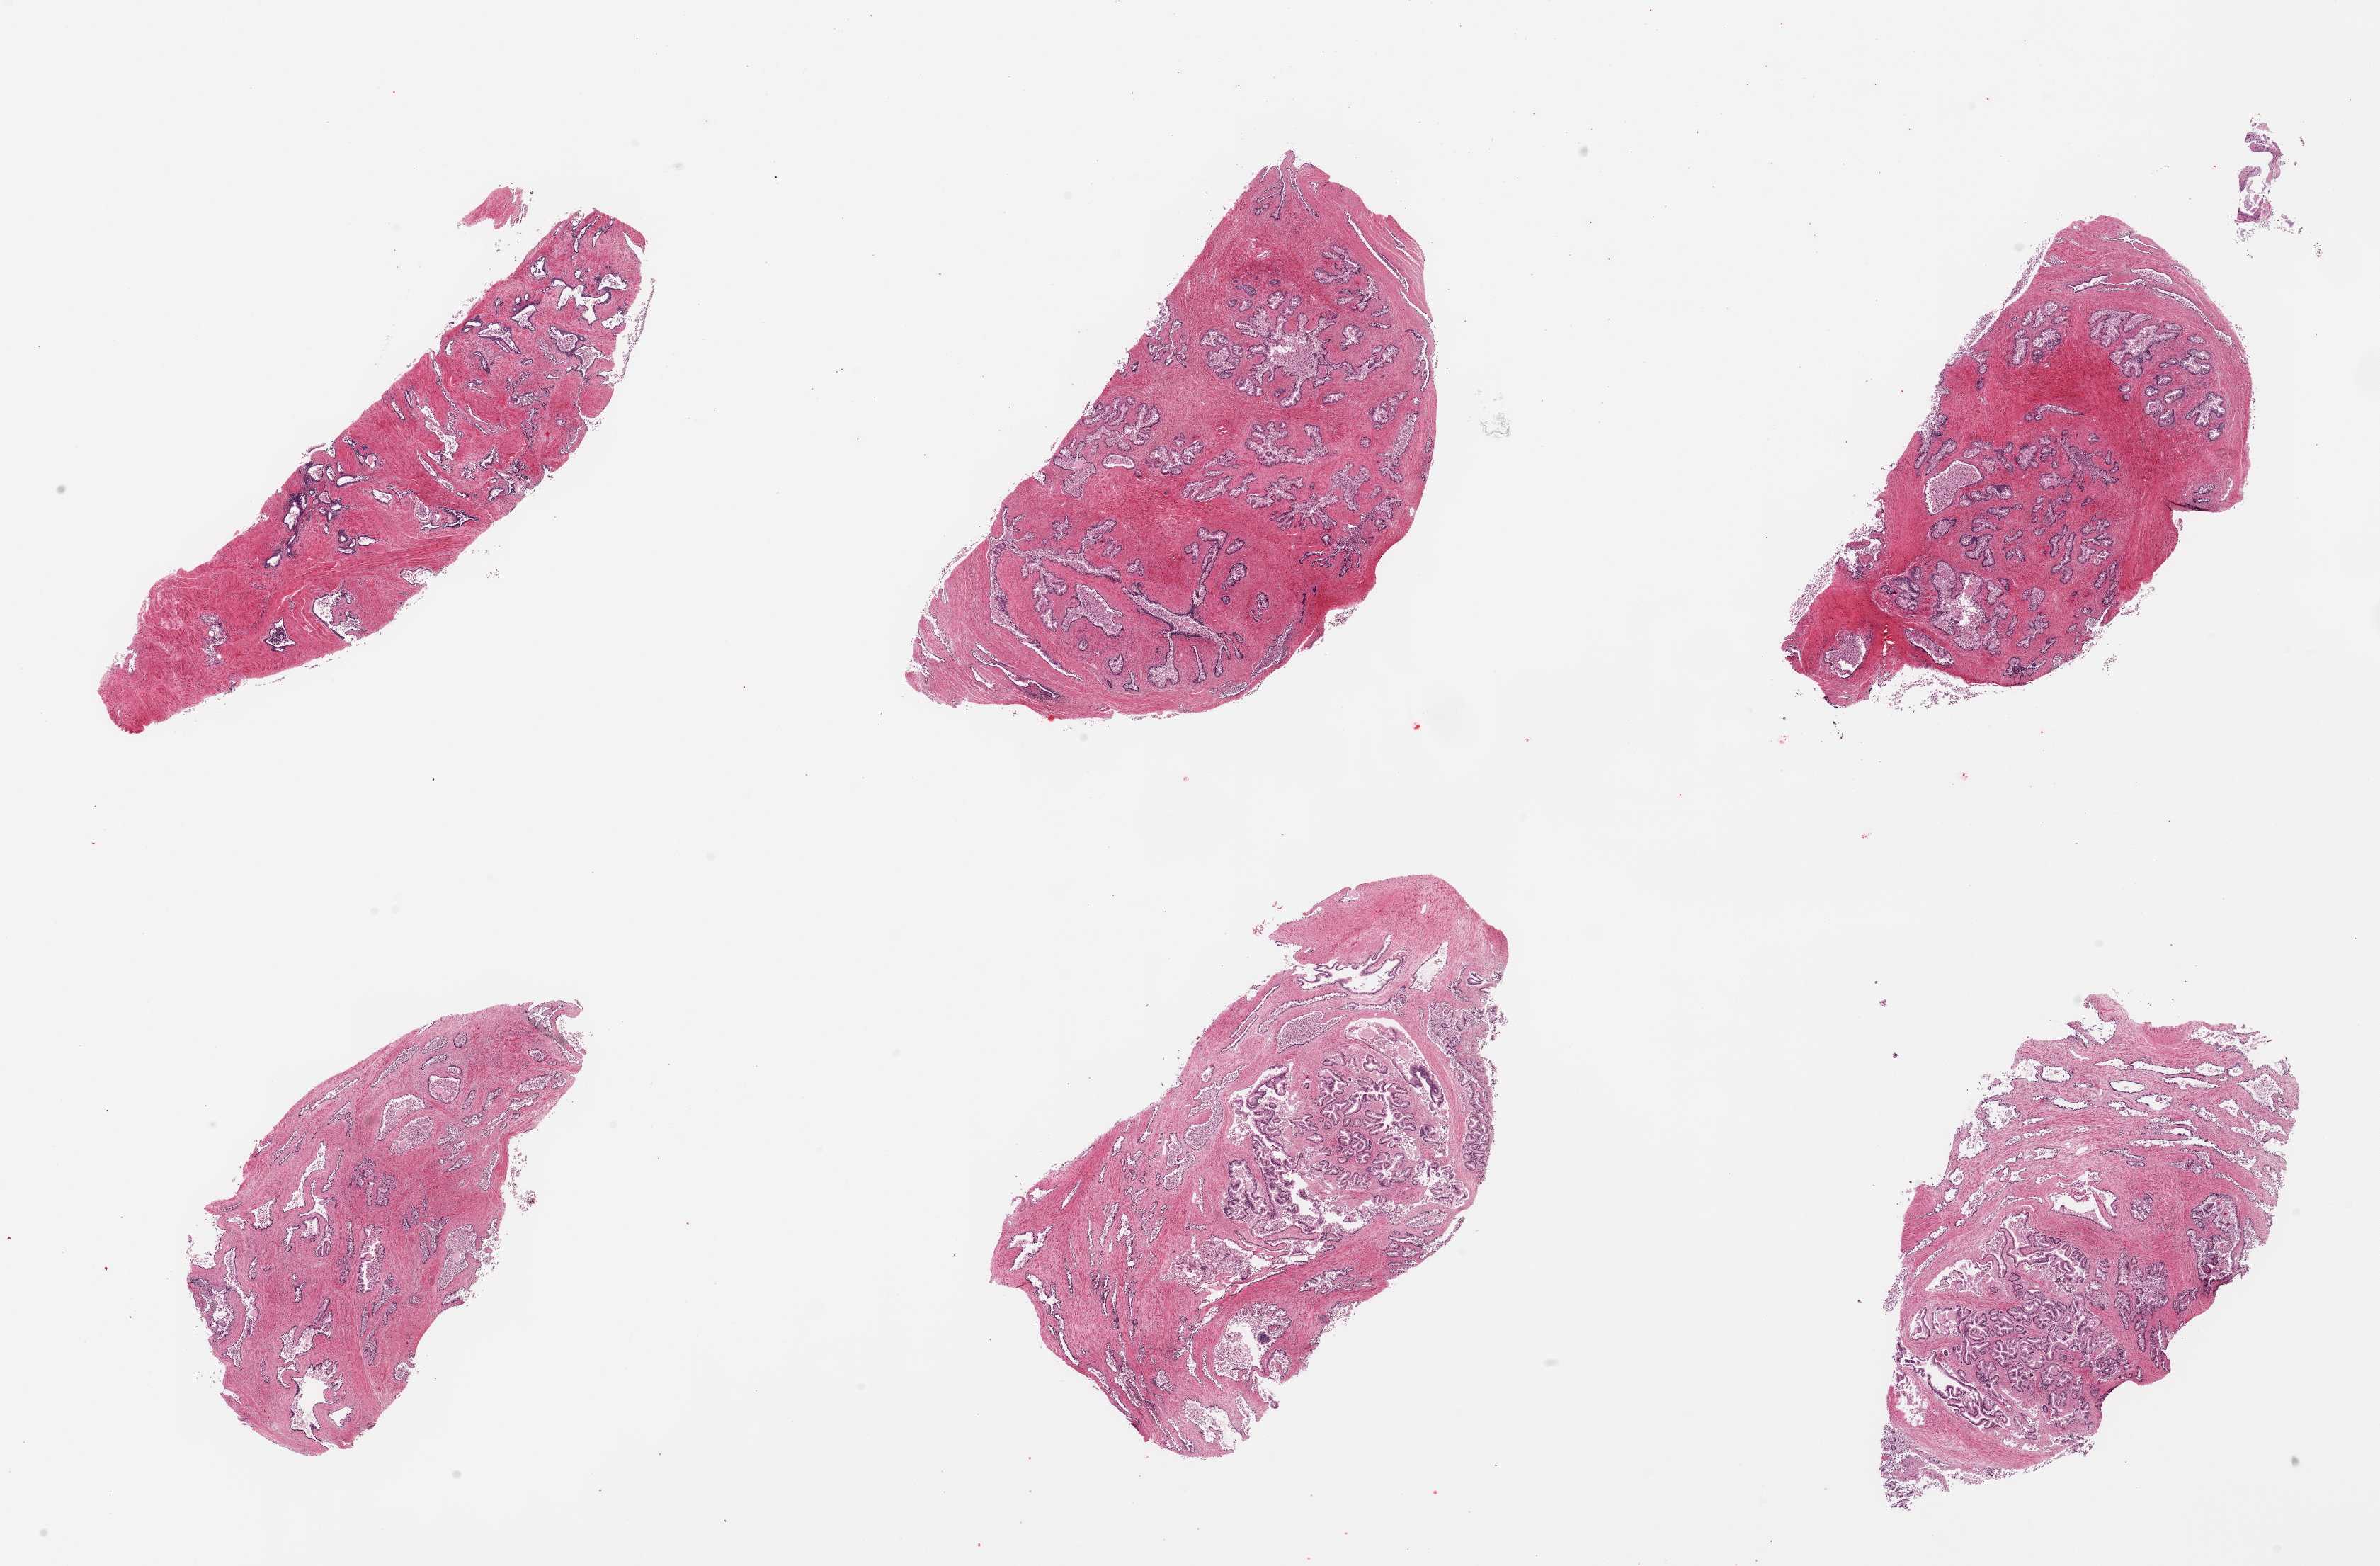
Whole-slide image, haematoxylin and eosin stain — low-resolution overview of the scanned area, about 26.6 x 17.5 mm; PAXgene-fixed paraffin-embedded (PFPE) section; section of prostate (target tissue); tissue donor sample. Male donor.
- reviewer comment on this tissue sample: 6 pieces; prostate, not pituitary, fibromuscular stroma and glands with sloughed epithelium